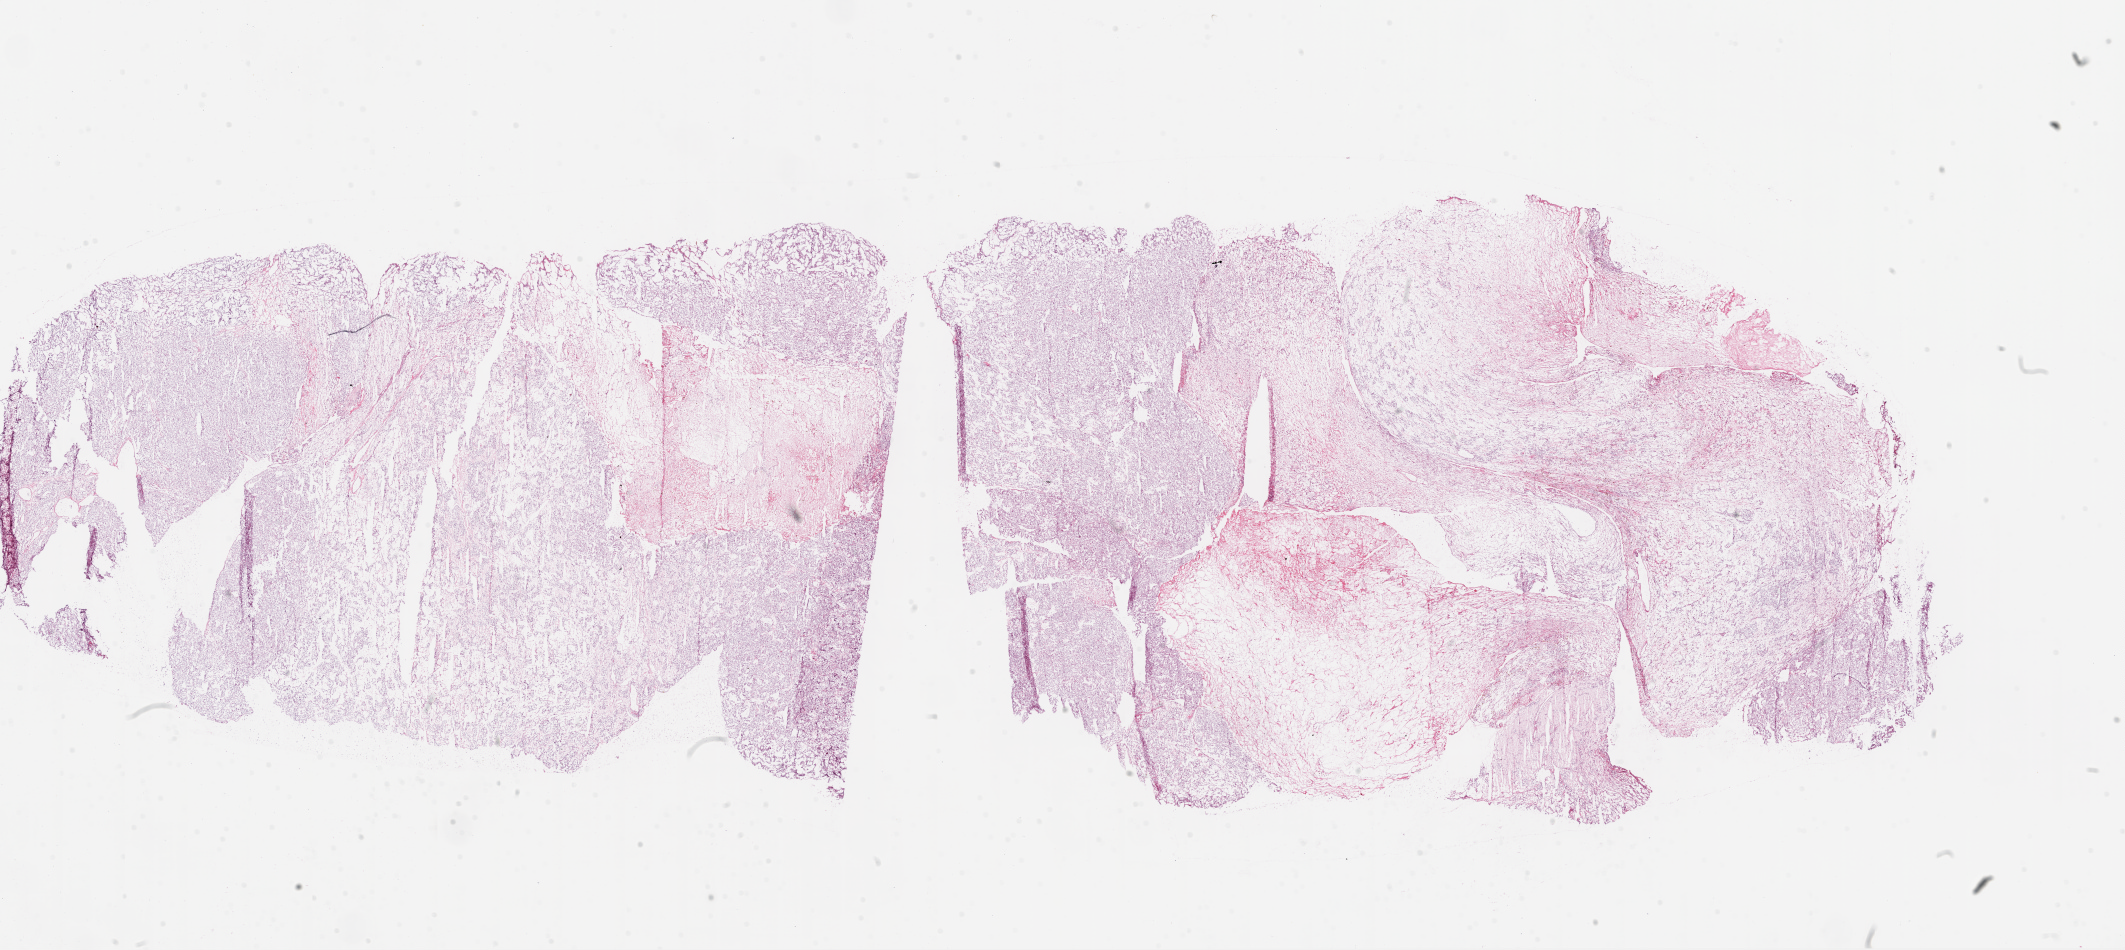
H&E whole-slide image — a low-resolution overview of the entire scanned area, about 34.1 x 15.2 mm, frozen section from the bottom of the tissue portion, kidney, primary tumour sample. Female patient; age at initial diagnosis 60 years. Histologic grade: G2 (moderately differentiated). Composition of this section per pathologist review: tumour cells 70%, tumour nuclei 80%, normal cells 0%, stromal cells 30%, necrosis 0%.
* laterality: right
* histologic diagnosis: Clear cell adenocarcinoma, NOS
* AJCC pathologic stage: I (7th edition)